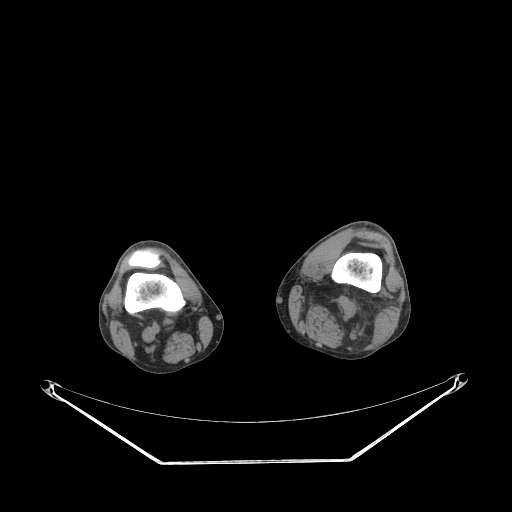
CT of an extremity soft-tissue mass (from a PET/CT study), one axial slice. Slice 196 of 267 in the series (ordered by position). Reconstruction kernel STANDARD. Soft-tissue window (W 400 / L 40 HU). 512 × 512 image matrix, field of view 500 × 500 mm. Male patient. From the clinical record (not read from this slice): histological type: undifferentiated pleomorphic liposarcoma; grade: high; site of the primary tumour: left thigh.
Annotated regions visible in this slice (expert contour drawn on MRI and transferred to this co-registered scan by the dataset authors):
- gross tumour volume including surrounding oedema: bounding box (x1, y1, x2, y2) in pixels: (299, 292, 373, 321)